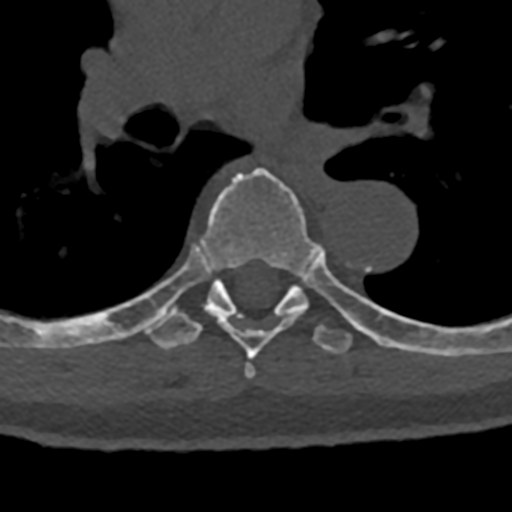
CT including the spine, one axial slice. Slice 791 of 797 in the series (ordered by position). Reconstruction kernel Br40s/3. 120 kVp. Bone window (W 1800 / L 400 HU). 0.5 mm slice thickness. 512 × 512 image matrix, field of view 160 × 160 mm. Patient: male, 74 years. From the clinical record (not read from this slice): primary cancer: renal.
Outlined on this slice (semi-automatic segmentation, software-assisted and operator-edited):
- T6 vertebra: bounding box [x1, y1, x2, y2] px = [144, 167, 318, 379]
- T7 vertebra: [70, 245, 432, 355]